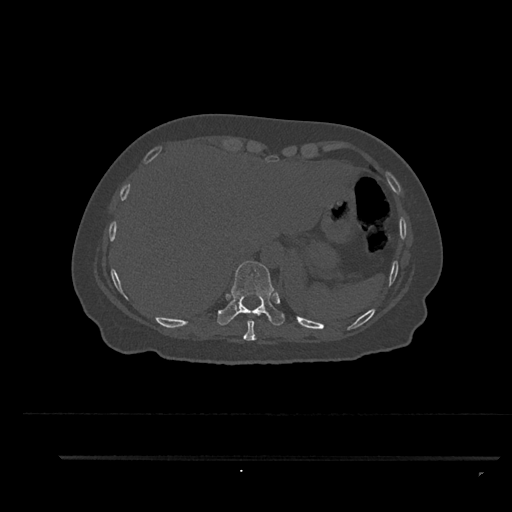
CT including the spine, one axial slice. Slice 376 of 797 in the series (ordered by position). Reconstruction kernel Br40s/3. 120 kVp. Bone window (W 1800 / L 400 HU). 0.5 mm slice thickness. 512 × 512 image matrix, field of view 408 × 408 mm. Patient: female, 44 years. From the clinical record (not read from this slice): primary cancer: renal.
Structures marked on this image (semi-automatically segmented with operator editing):
- T10 vertebra: bounding box [x1, y1, x2, y2] px = [217, 260, 285, 326]
- T9 vertebra: [243, 321, 257, 341]